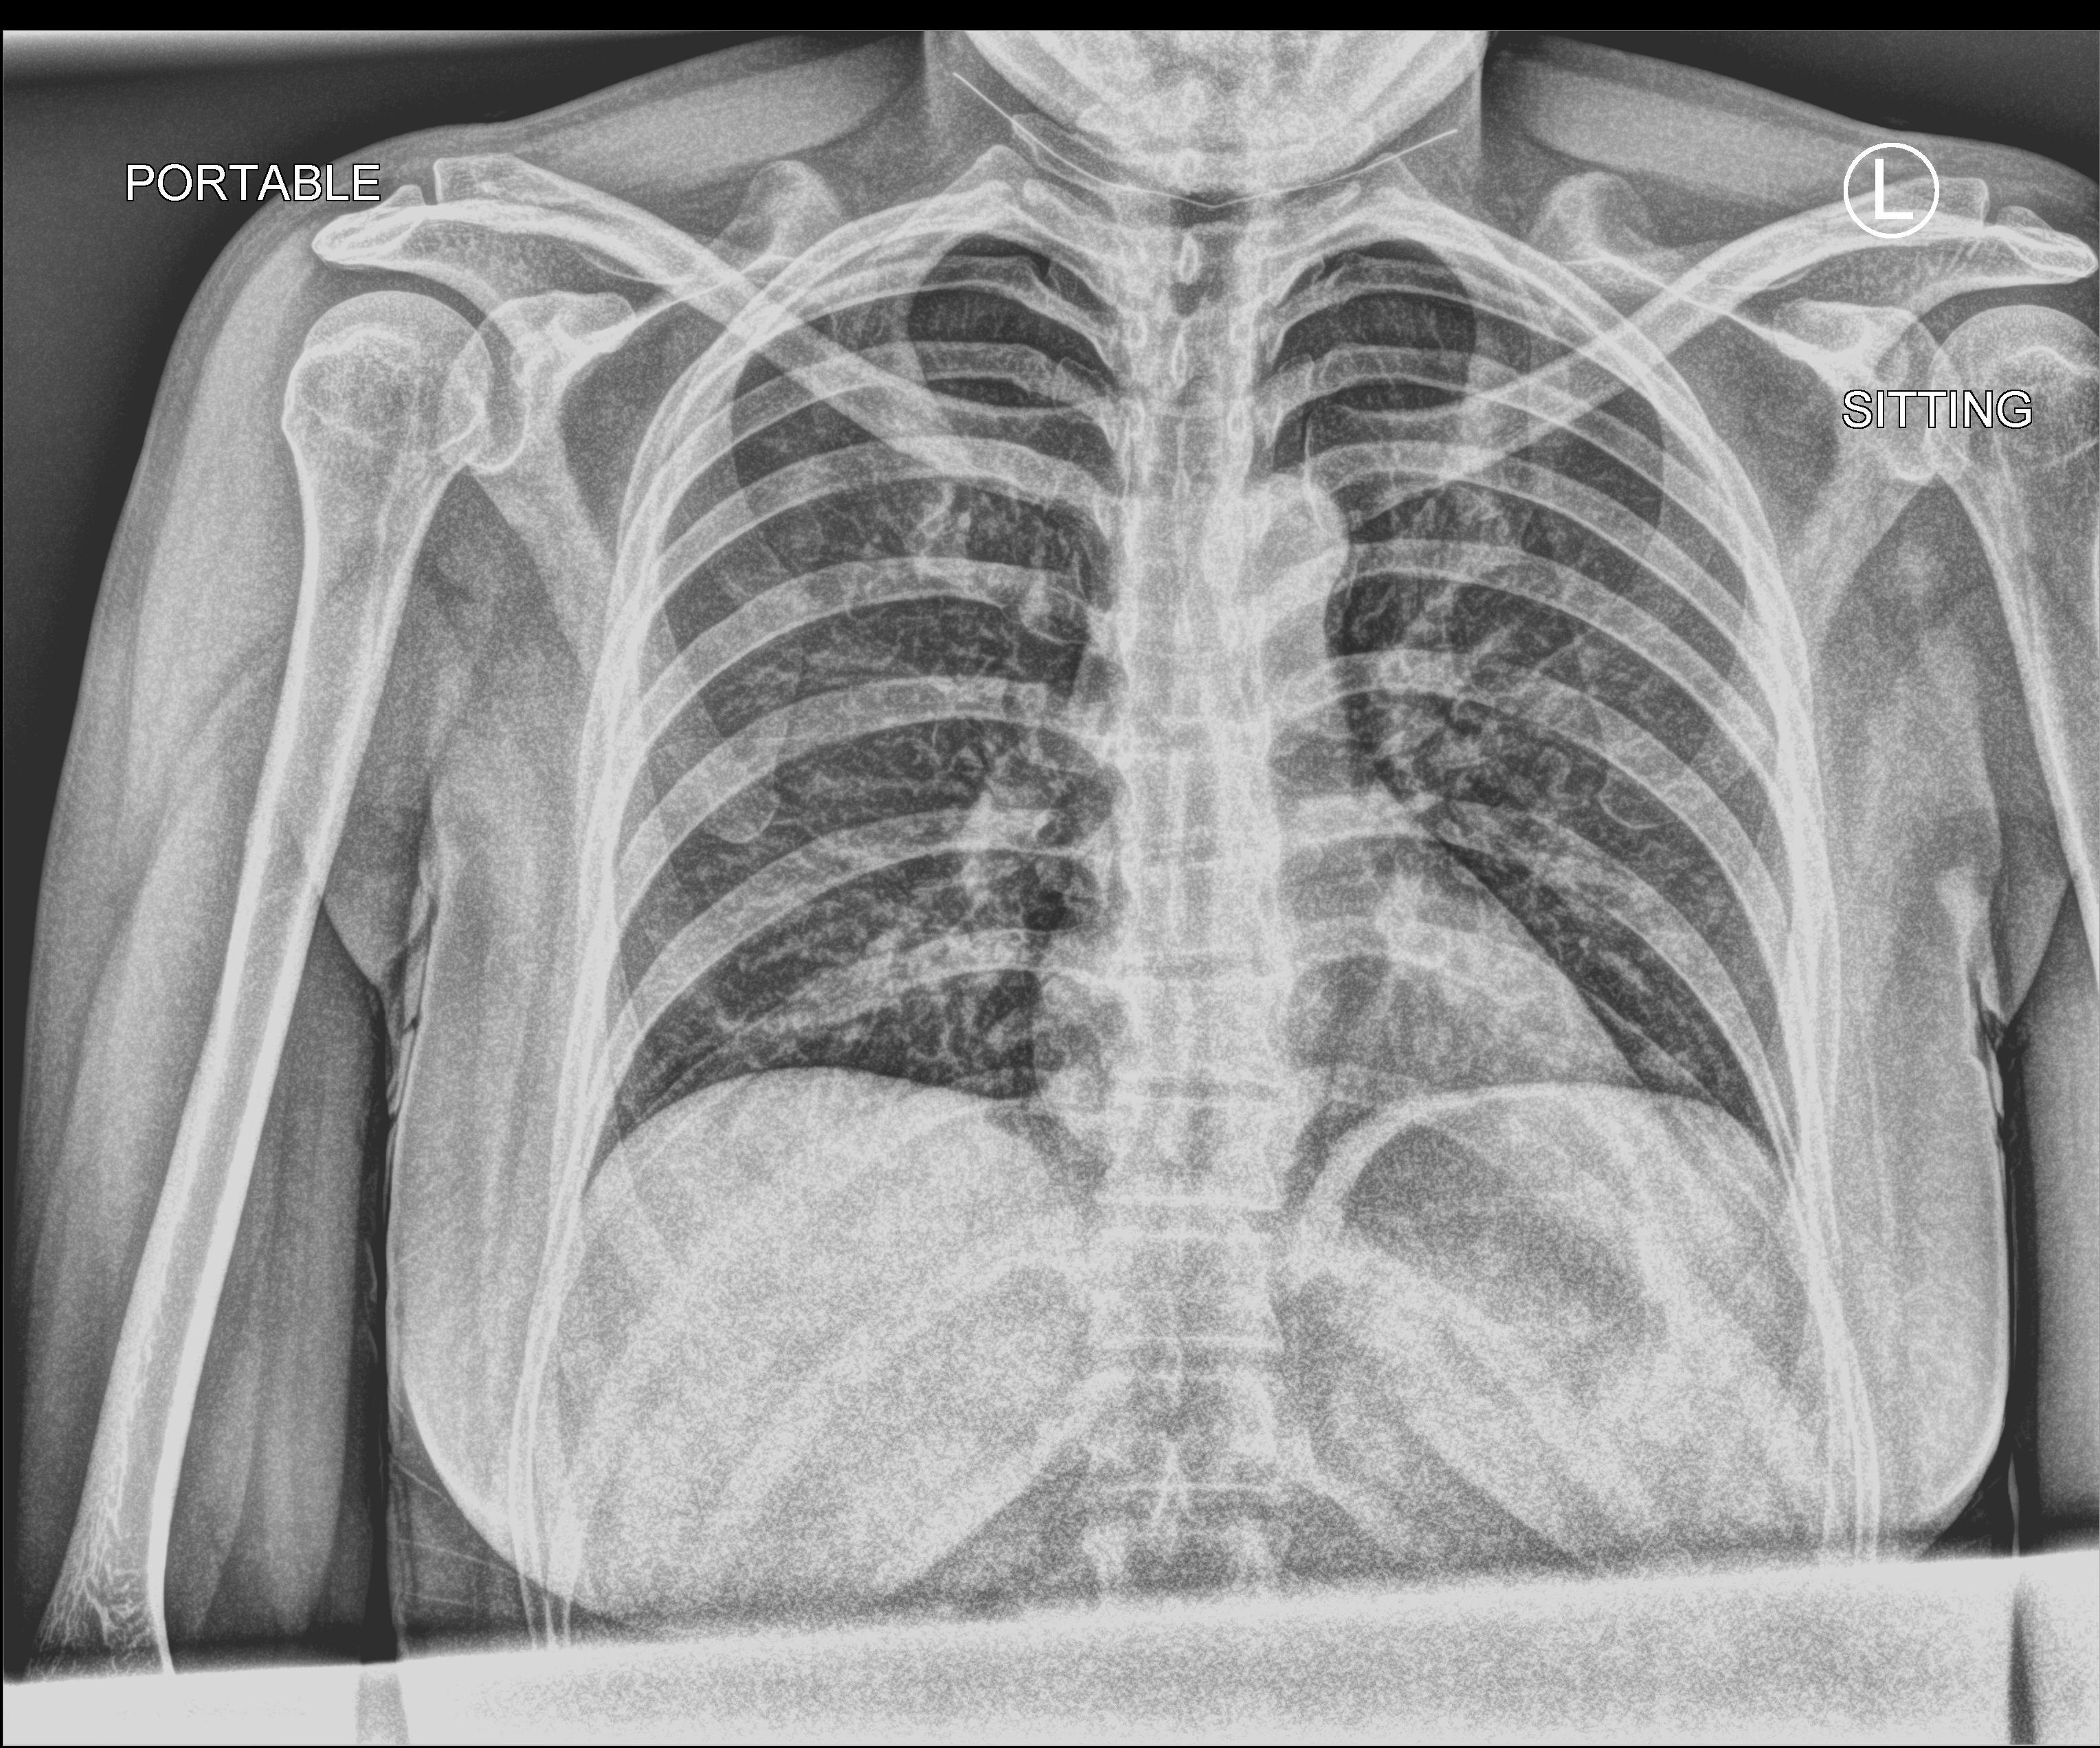
Portable chest radiograph, anteroposterior (AP) projection. Female patient hospitalised with COVID-19, age 18–59 years.
Hospital-stay facts (about this admission, not read from this image; timing relative to this image not recorded): smoking status (admission record): current; admitted to intensive care during this hospital stay: no.